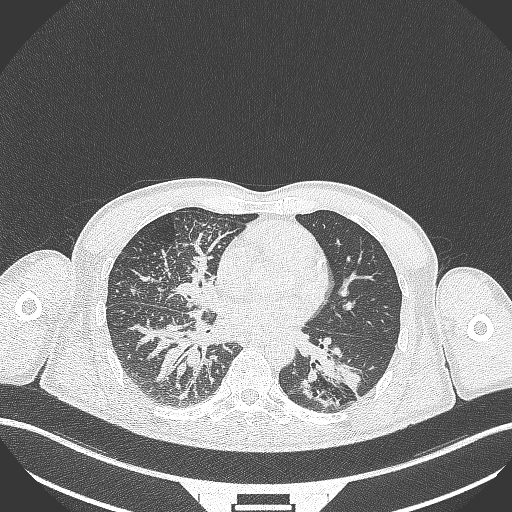
Chest CT, one axial slice. Reconstruction kernel B70f. 120 kVp. Lung window (W 1500 / L -600 HU). 1 mm slice thickness. 512 × 512 image matrix, field of view 400 × 400 mm. Patient: male, 49 years. Case-level facts recorded for this patient, not image findings: clinical TNM (as recorded): T2b N1 M0.
Annotated regions visible in this slice (bounding box drawn by a radiologist):
- lung tumour (recorded histology: adenocarcinoma): bounding box [x1, y1, x2, y2] px = [295, 349, 364, 411]